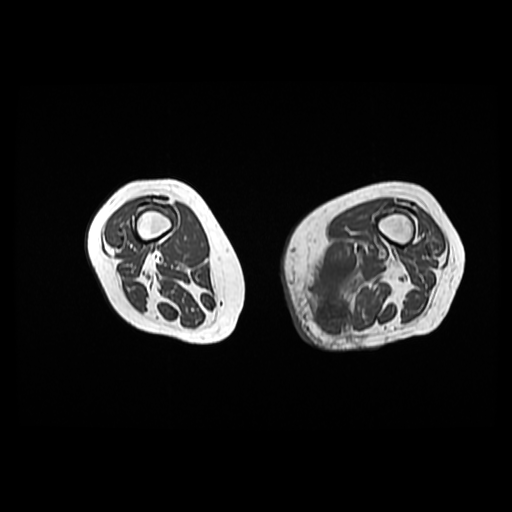
MRI of an extremity soft-tissue mass, one axial slice. Slice 23 of 42 in the series (ordered by position). 512 × 512 image matrix, field of view 420 × 420 mm. Female patient. Case-level facts recorded for this patient, not image findings: histological type: pleomorphic leiomyosarcoma; grade: high; site of the primary tumour: left thigh.
Annotated regions visible in this slice (outlined manually by an expert reader):
- gross tumour volume including surrounding oedema: bounding box (x1, y1, x2, y2) in pixels: (306, 250, 400, 334)
- gross tumour volume (mass): (315, 297, 354, 334)